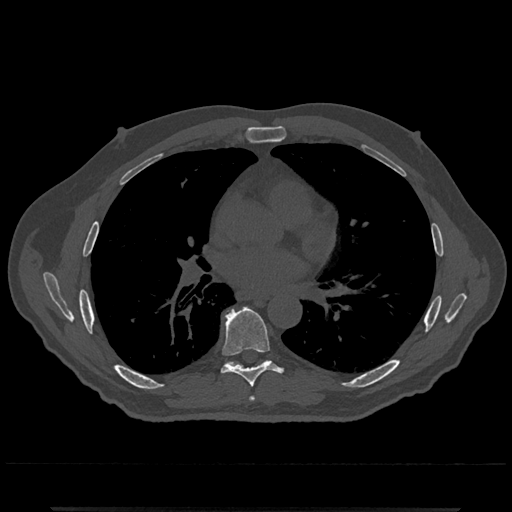
CT including the spine, one axial slice; position 716 of 797 along the scan axis; reconstruction kernel Br40s/3; bone window (W 1800 / L 400 HU); 0.5 mm slice thickness; 512 × 512 image matrix, field of view 393 × 393 mm. Male patient, age 67 years. Case-level facts recorded for this patient, not image findings: primary cancer: prostate.
Structures marked on this image (semi-automatic segmentation, software-assisted and operator-edited):
- T6 vertebra: bounding box <249,396,255,402> (left, top, right, bottom; pixels)
- T7 vertebra: <221,308,280,388>
- T8 vertebra: <226,360,268,365>